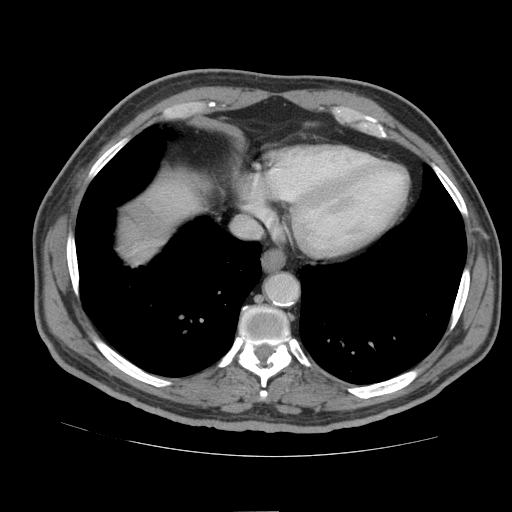
Contrast-enhanced abdominal CT (liver protocol), one axial slice. Slice 81 of 105 in the series (ordered by position). 140 kVp. Soft-tissue window (W 400 / L 40 HU). 512 × 512 image matrix, field of view 380 × 380 mm. Case-level facts recorded for this patient, not image findings: diagnosis: hepatocellular carcinoma (patient treated with transarterial chemoembolisation; whether this scan precedes or follows treatment is not stated here); TNM stage (as recorded): Stage-IIIB; Child-Pugh class: A; tumour nodularity: multinodular.
Structures marked on this image (semi-automatically segmented with operator editing):
- liver parenchyma outside the tumour (the mass and vessels are separate outlines, so this box may not span the whole liver): box from (x=122, y=180) to (x=198, y=260) px